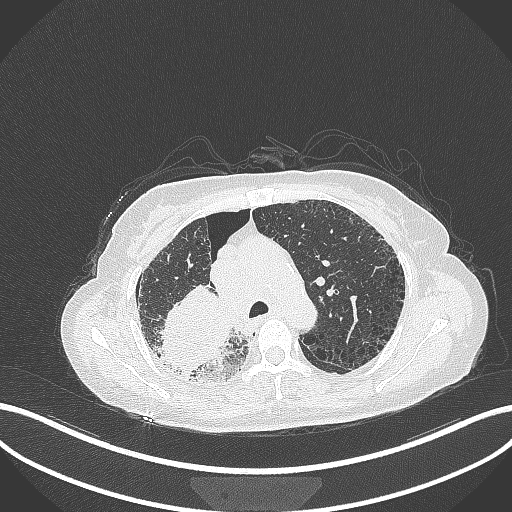
Chest CT, one axial slice; position 243 of 408 along the scan axis; reconstruction kernel B70f; lung window (W 1500 / L -600 HU); 1 mm slice thickness; 512 × 512 image matrix, field of view 400 × 400 mm. Female patient, age 64 years. Case-level facts recorded for this patient, not image findings: clinical TNM (as recorded): T3 N3 M0.
Structures marked on this image (rectangle marked by the reading radiologist):
- lung tumour (recorded histology: squamous cell carcinoma): bounding box [x1, y1, x2, y2] px = [159, 282, 233, 375]